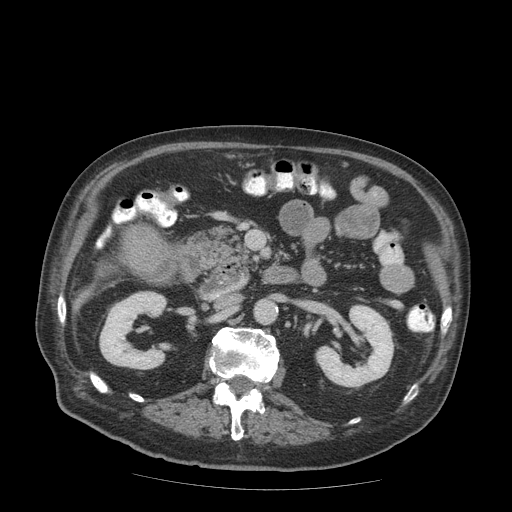
Contrast-enhanced abdominal CT (liver protocol), one axial slice. Slice 22 of 99 in the series (ordered by position). 140 kVp. Soft-tissue window (W 400 / L 40 HU). 2.5 mm slice thickness. 512 × 512 image matrix. Case-level facts recorded for this patient, not image findings: diagnosis: hepatocellular carcinoma (patient treated with transarterial chemoembolisation; whether this scan precedes or follows treatment is not stated here); TNM stage (as recorded): Stage-IIIB; Child-Pugh class: A; tumour differentiation: well differentiated.
Annotated regions visible in this slice (semi-automatic segmentation, software-assisted and operator-edited):
- mass: box from (x=125, y=228) to (x=160, y=267) px